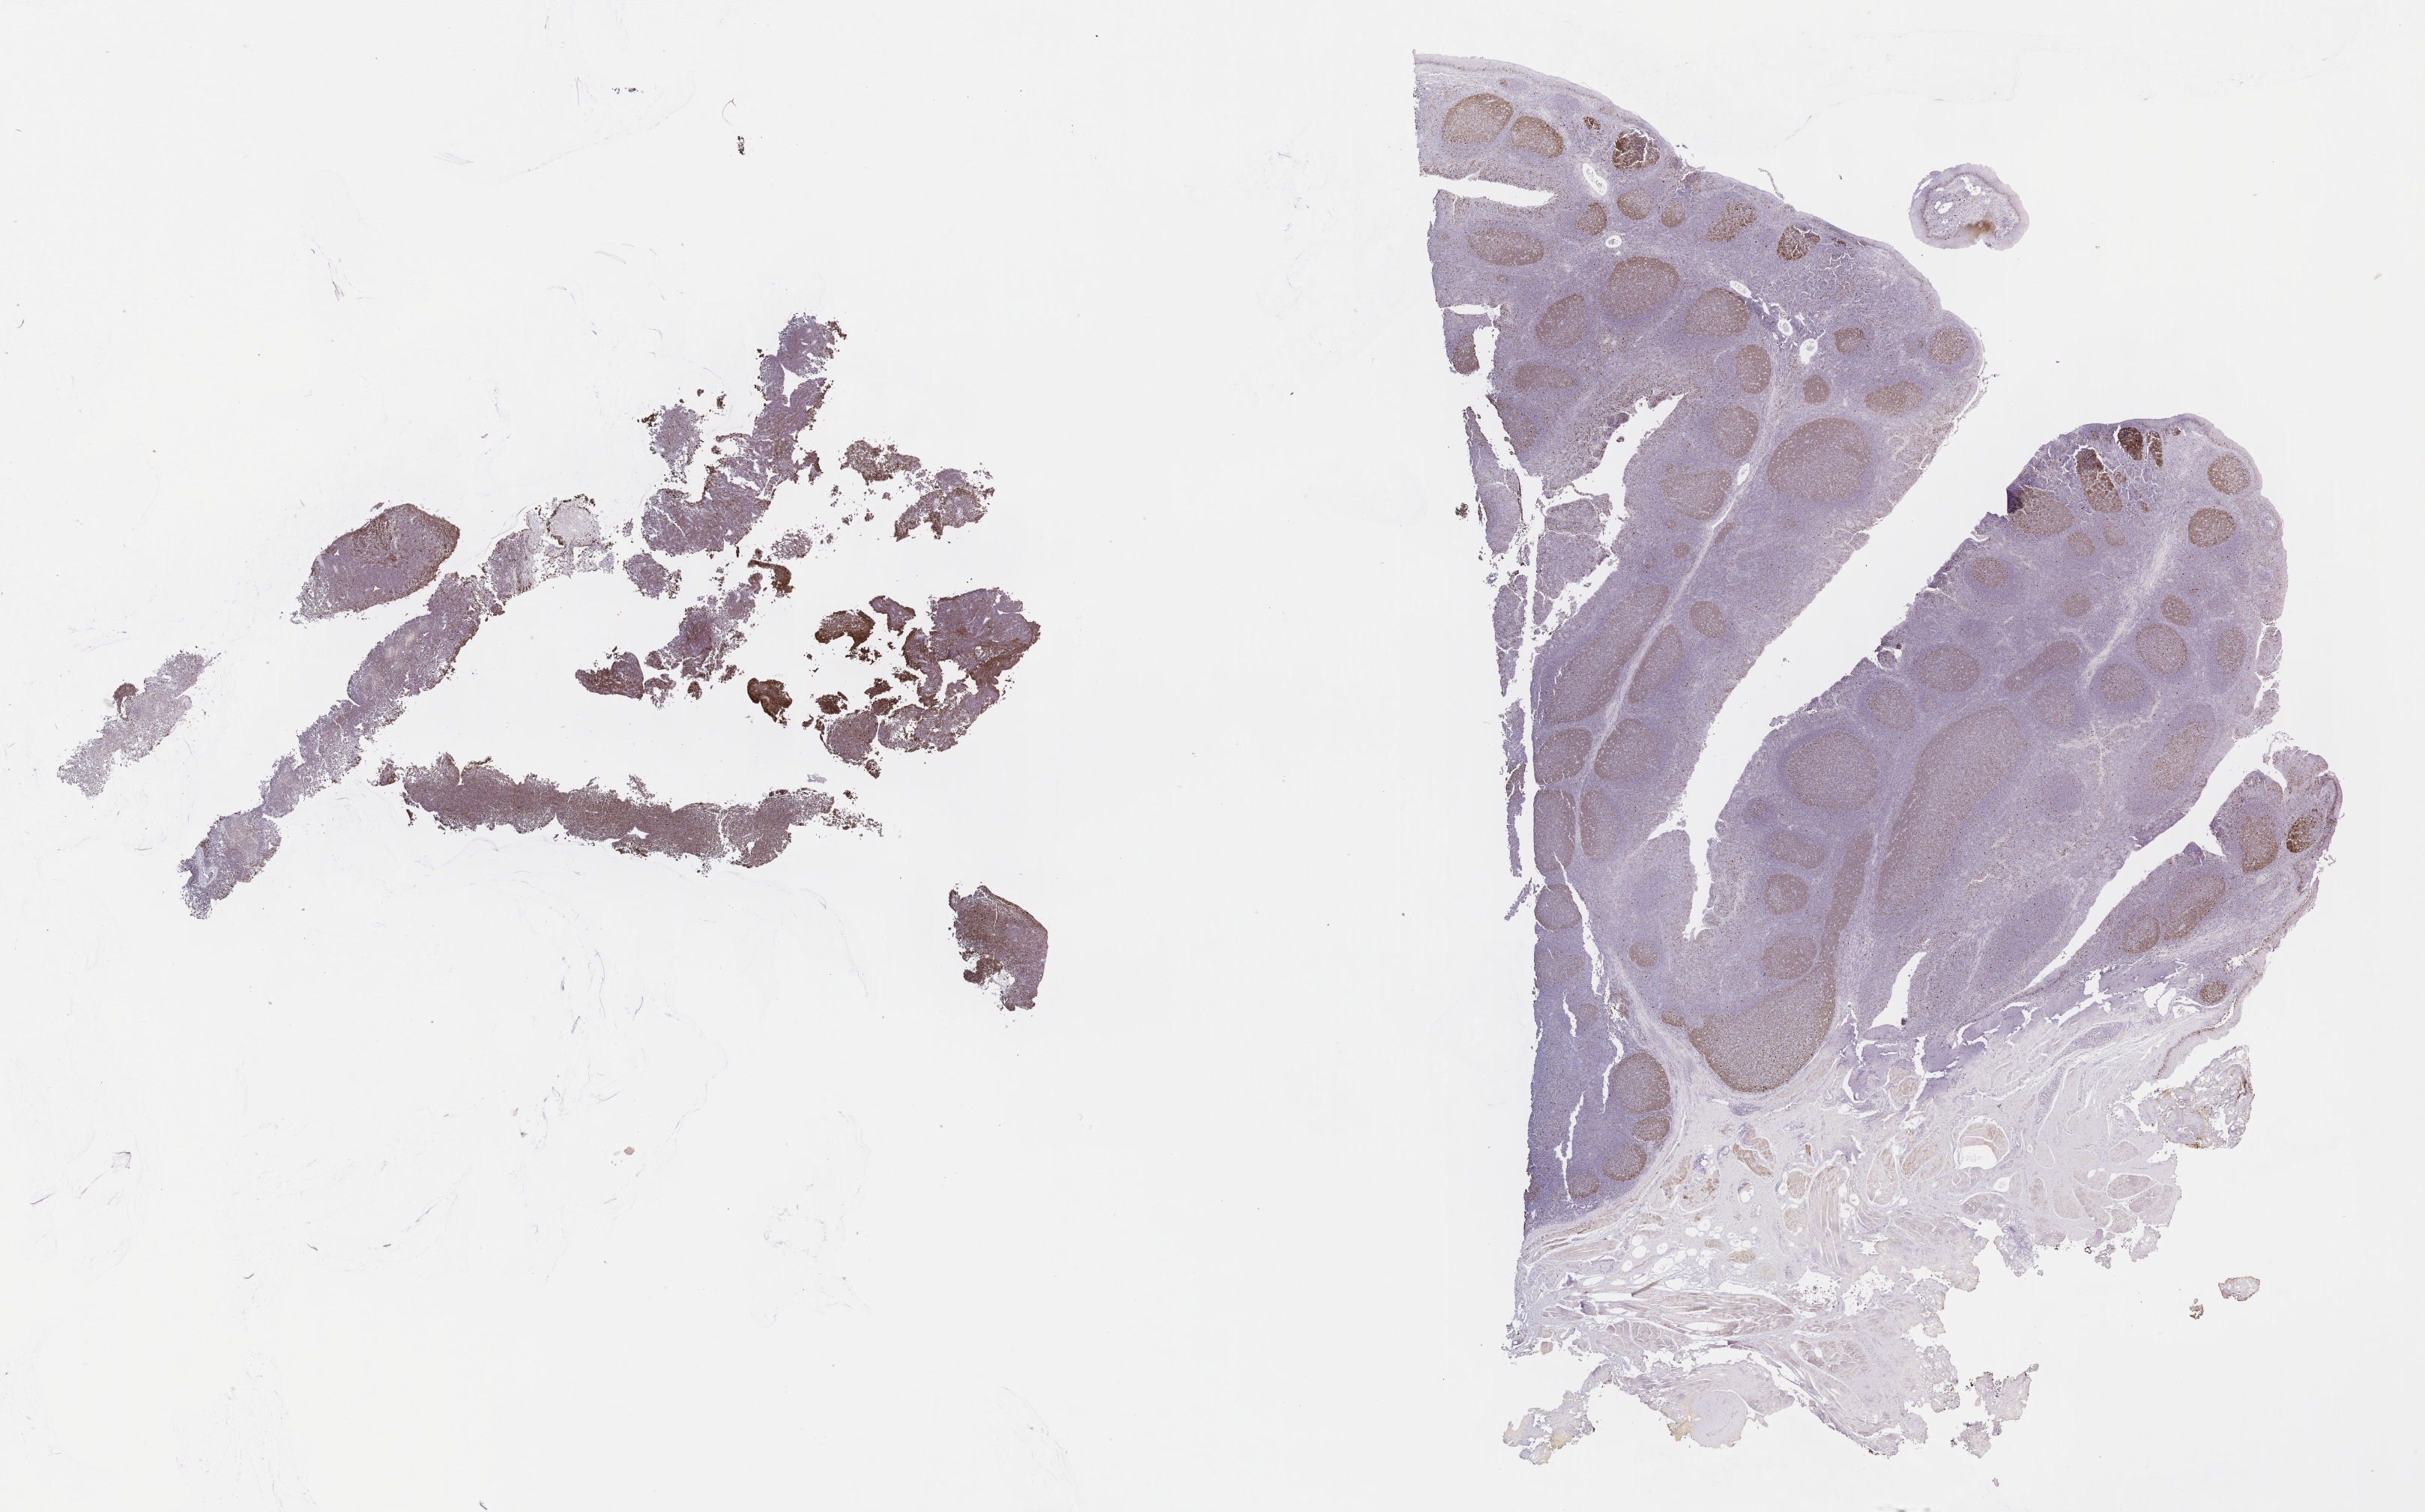
IHC for Ki-67, whole-slide image — shown as a low-resolution overview of the whole scanned area (about 26.2 x 16.3 mm), tumor tissue, site: kidney. Male, age 3 years at initial diagnosis.
* histologic diagnosis: Burkitt lymphoma, NOS